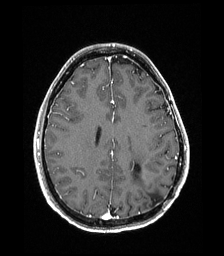
Brain MRI from a brain-tumour surgery series, one axial slice. Slice 73 of 192 in the series (ordered by position). T1-weighted post-contrast. 1 mm slice thickness. 224 × 256 image matrix, field of view 224 × 256 mm. From the clinical record (not read from this slice): histopathology: Low grade glioma; IDH mutation: no; tumour location: Left Parieto-Occipital Intraventricular.
Outlined on this slice (outlined manually by an expert reader):
- previous resection cavity: bounding box (x1, y1, x2, y2) in pixels: (133, 167, 159, 204)